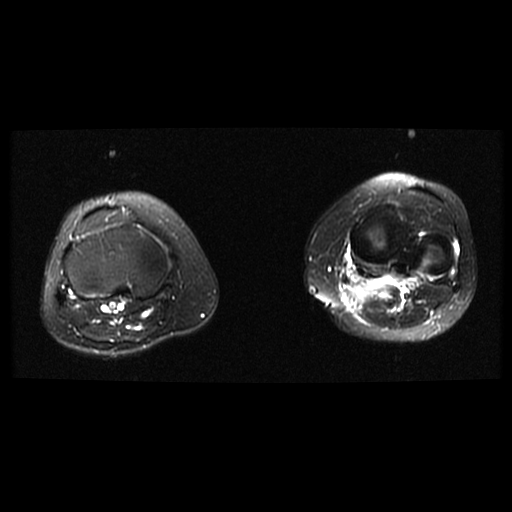
MRI of an extremity soft-tissue mass, one axial slice; position 26 of 38 along the scan axis; T2-weighted fat-saturated; 512 × 512 image matrix, field of view 330 × 330 mm. Female patient. Case-level facts recorded for this patient, not image findings: histological type: extraskeletal high grade osteogenic sarcoma; grade: high; site of the primary tumour: left calf.
Structures marked on this image (expert manual segmentation):
- gross tumour volume (mass): box from (x=356, y=282) to (x=375, y=301) px